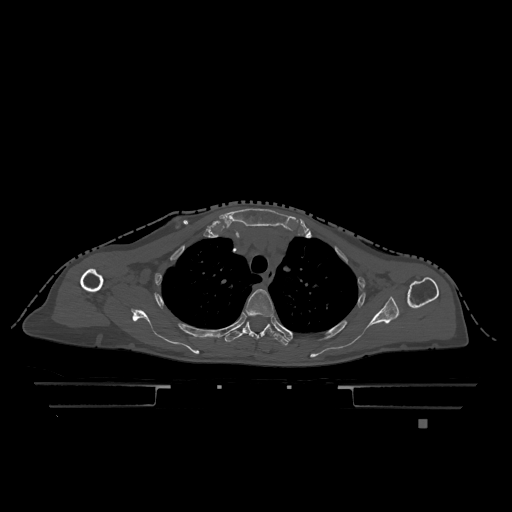
CT including the spine, one axial slice; position 902 of 1317 along the scan axis; bone window (W 1800 / L 400 HU); 512 × 512 image matrix, field of view 500 × 500 mm. Patient: female, 74 years. Case-level facts recorded for this patient, not image findings: primary cancer: lung; vertebrae with lytic lesions (as recorded): T1, T4, T5, T6, L4, L5.
Annotated regions visible in this slice (semi-automatic segmentation, software-assisted and operator-edited):
- T3 vertebra: bounding box <246,289,274,317> (left, top, right, bottom; pixels)
- T4 vertebra: <224,314,293,346>